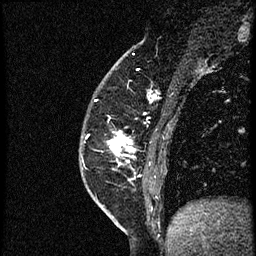
Breast MRI (dynamic contrast-enhanced), one sagittal slice. Slice 18 of 56 in the series (ordered by position). Dynamic contrast-enhanced study with each time point stored as its own series, time point 2 of 4 at this slice position (early post-contrast, ordered by acquisition time). 1.5 T. TE 4.2 ms, TR 18.9 ms. 2 mm slice thickness. 256 × 256 image matrix, field of view 200 × 200 mm. Female patient. From the clinical record (not read from this slice): setting: breast cancer imaged before/during neoadjuvant chemotherapy; receptor status: HER2-positive.
Structures marked on this image (semi-automatic segmentation, software-assisted and operator-edited):
- analysis volume of interest (the breast-tissue region the enhancement analysis was run in; not a lesion): bounding box [x1, y1, x2, y2] px = [111, 85, 174, 189]
- tumour enhancement mask (voxels above the 100 % enhancement threshold inside the analysis volume of interest): [111, 134, 134, 164]